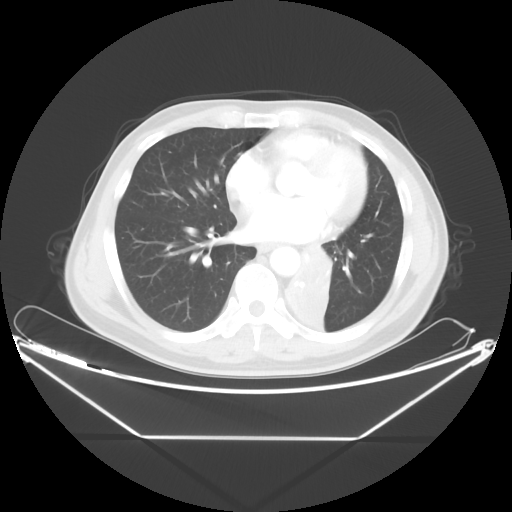
Chest CT, one axial slice. Position 18 of 48 along the scan axis. Reconstruction kernel STANDARD. Lung window (W 1500 / L -600 HU). 5 mm slice thickness. 512 × 512 image matrix. Patient: male, 58 years. From the clinical record (not read from this slice): clinical TNM (as recorded): T3 N3 M0.
Annotated regions visible in this slice (rectangle marked by the reading radiologist):
- lung tumour (recorded histology: squamous cell carcinoma): bounding box <280,246,343,332> (left, top, right, bottom; pixels)